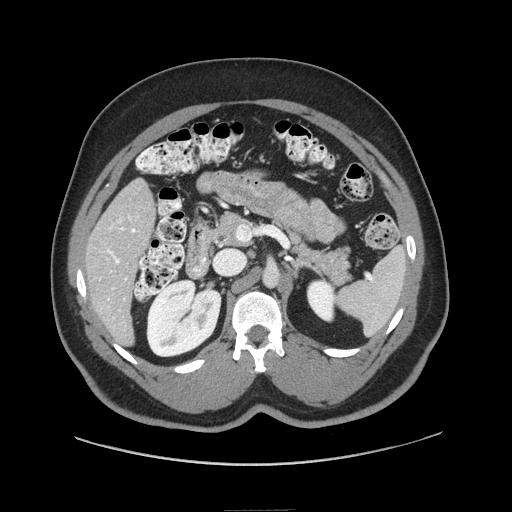
Contrast-enhanced abdominal CT (liver protocol), one axial slice; position 33 of 87 along the scan axis; reconstruction kernel STANDARD; 140 kVp; soft-tissue window (W 400 / L 40 HU); 2.5 mm slice thickness; 512 × 512 image matrix. Case-level facts recorded for this patient, not image findings: diagnosis: hepatocellular carcinoma (patient treated with transarterial chemoembolisation; whether this scan precedes or follows treatment is not stated here); TNM stage (as recorded): Stage-II; Child-Pugh class: A; tumour nodularity: uninodular.
Outlined on this slice (semi-automatically segmented with operator editing):
- liver parenchyma outside the tumour (the mass and vessels are separate outlines, so this box may not span the whole liver): box from (x=86, y=178) to (x=154, y=344) px
- liver vessels: (x=99, y=216)–(x=138, y=324)